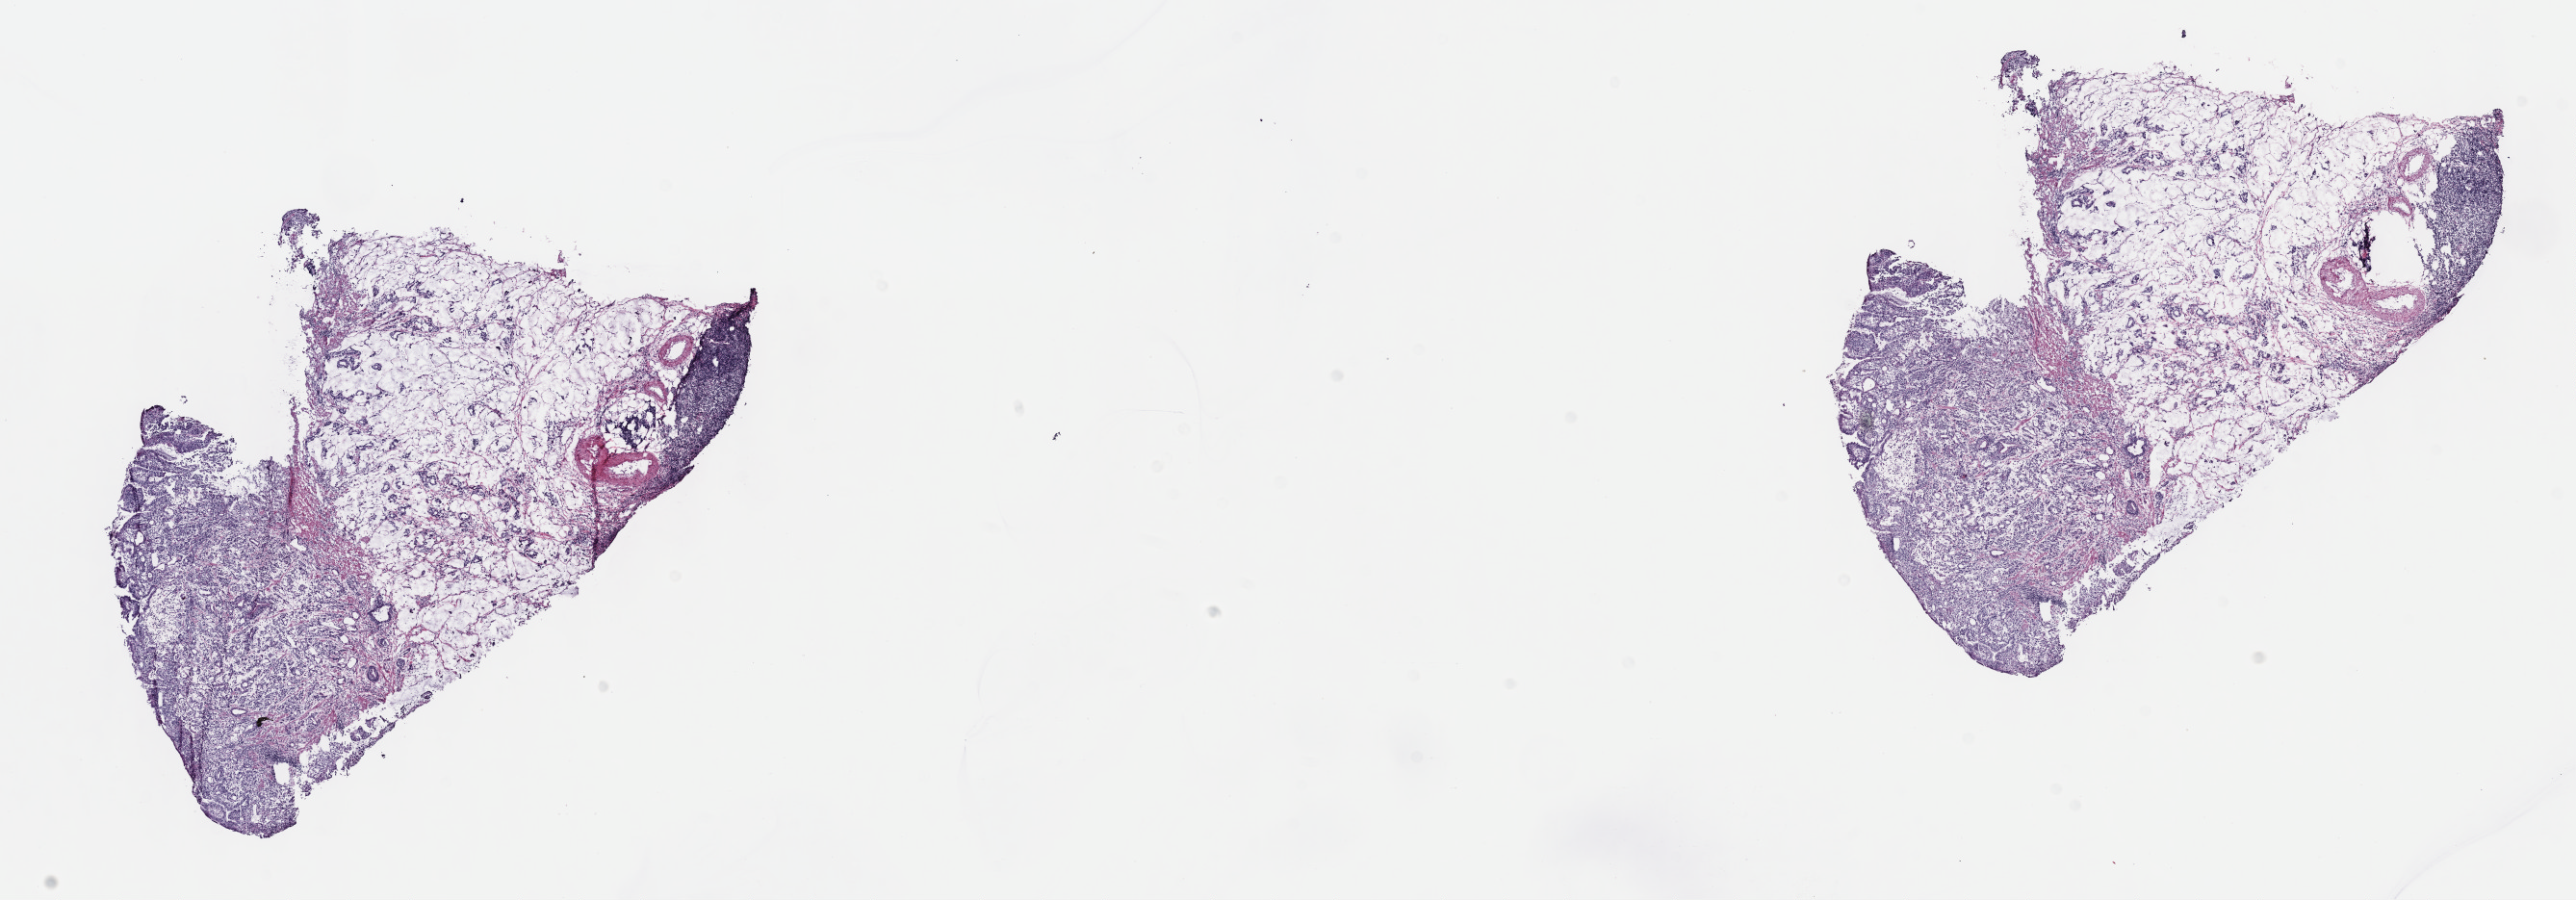
Hematoxylin and eosin (H&E) stained whole-slide image, shown as a low-resolution overview of the whole scanned area (about 21.6 x 7.6 mm, slide scanned at 40x); frozen section from the top of the tissue portion; stomach, primary tumour sample. Male, age 77 years at initial diagnosis. Histologic grade: G2 (moderately differentiated). Pathologist review of this section (percent, as recorded): tumour cells 60%, tumour nuclei 60%, normal cells 0%, stromal cells 30%, necrosis 10%. Infiltration values recorded for this section: lymphocyte infiltration 40%, monocyte infiltration 20%, neutrophil infiltration 20%.
Lymph nodes positive (case pathology): 2 of 26 examined. Diagnosis: Adenocarcinoma, NOS (cardia, NOS).